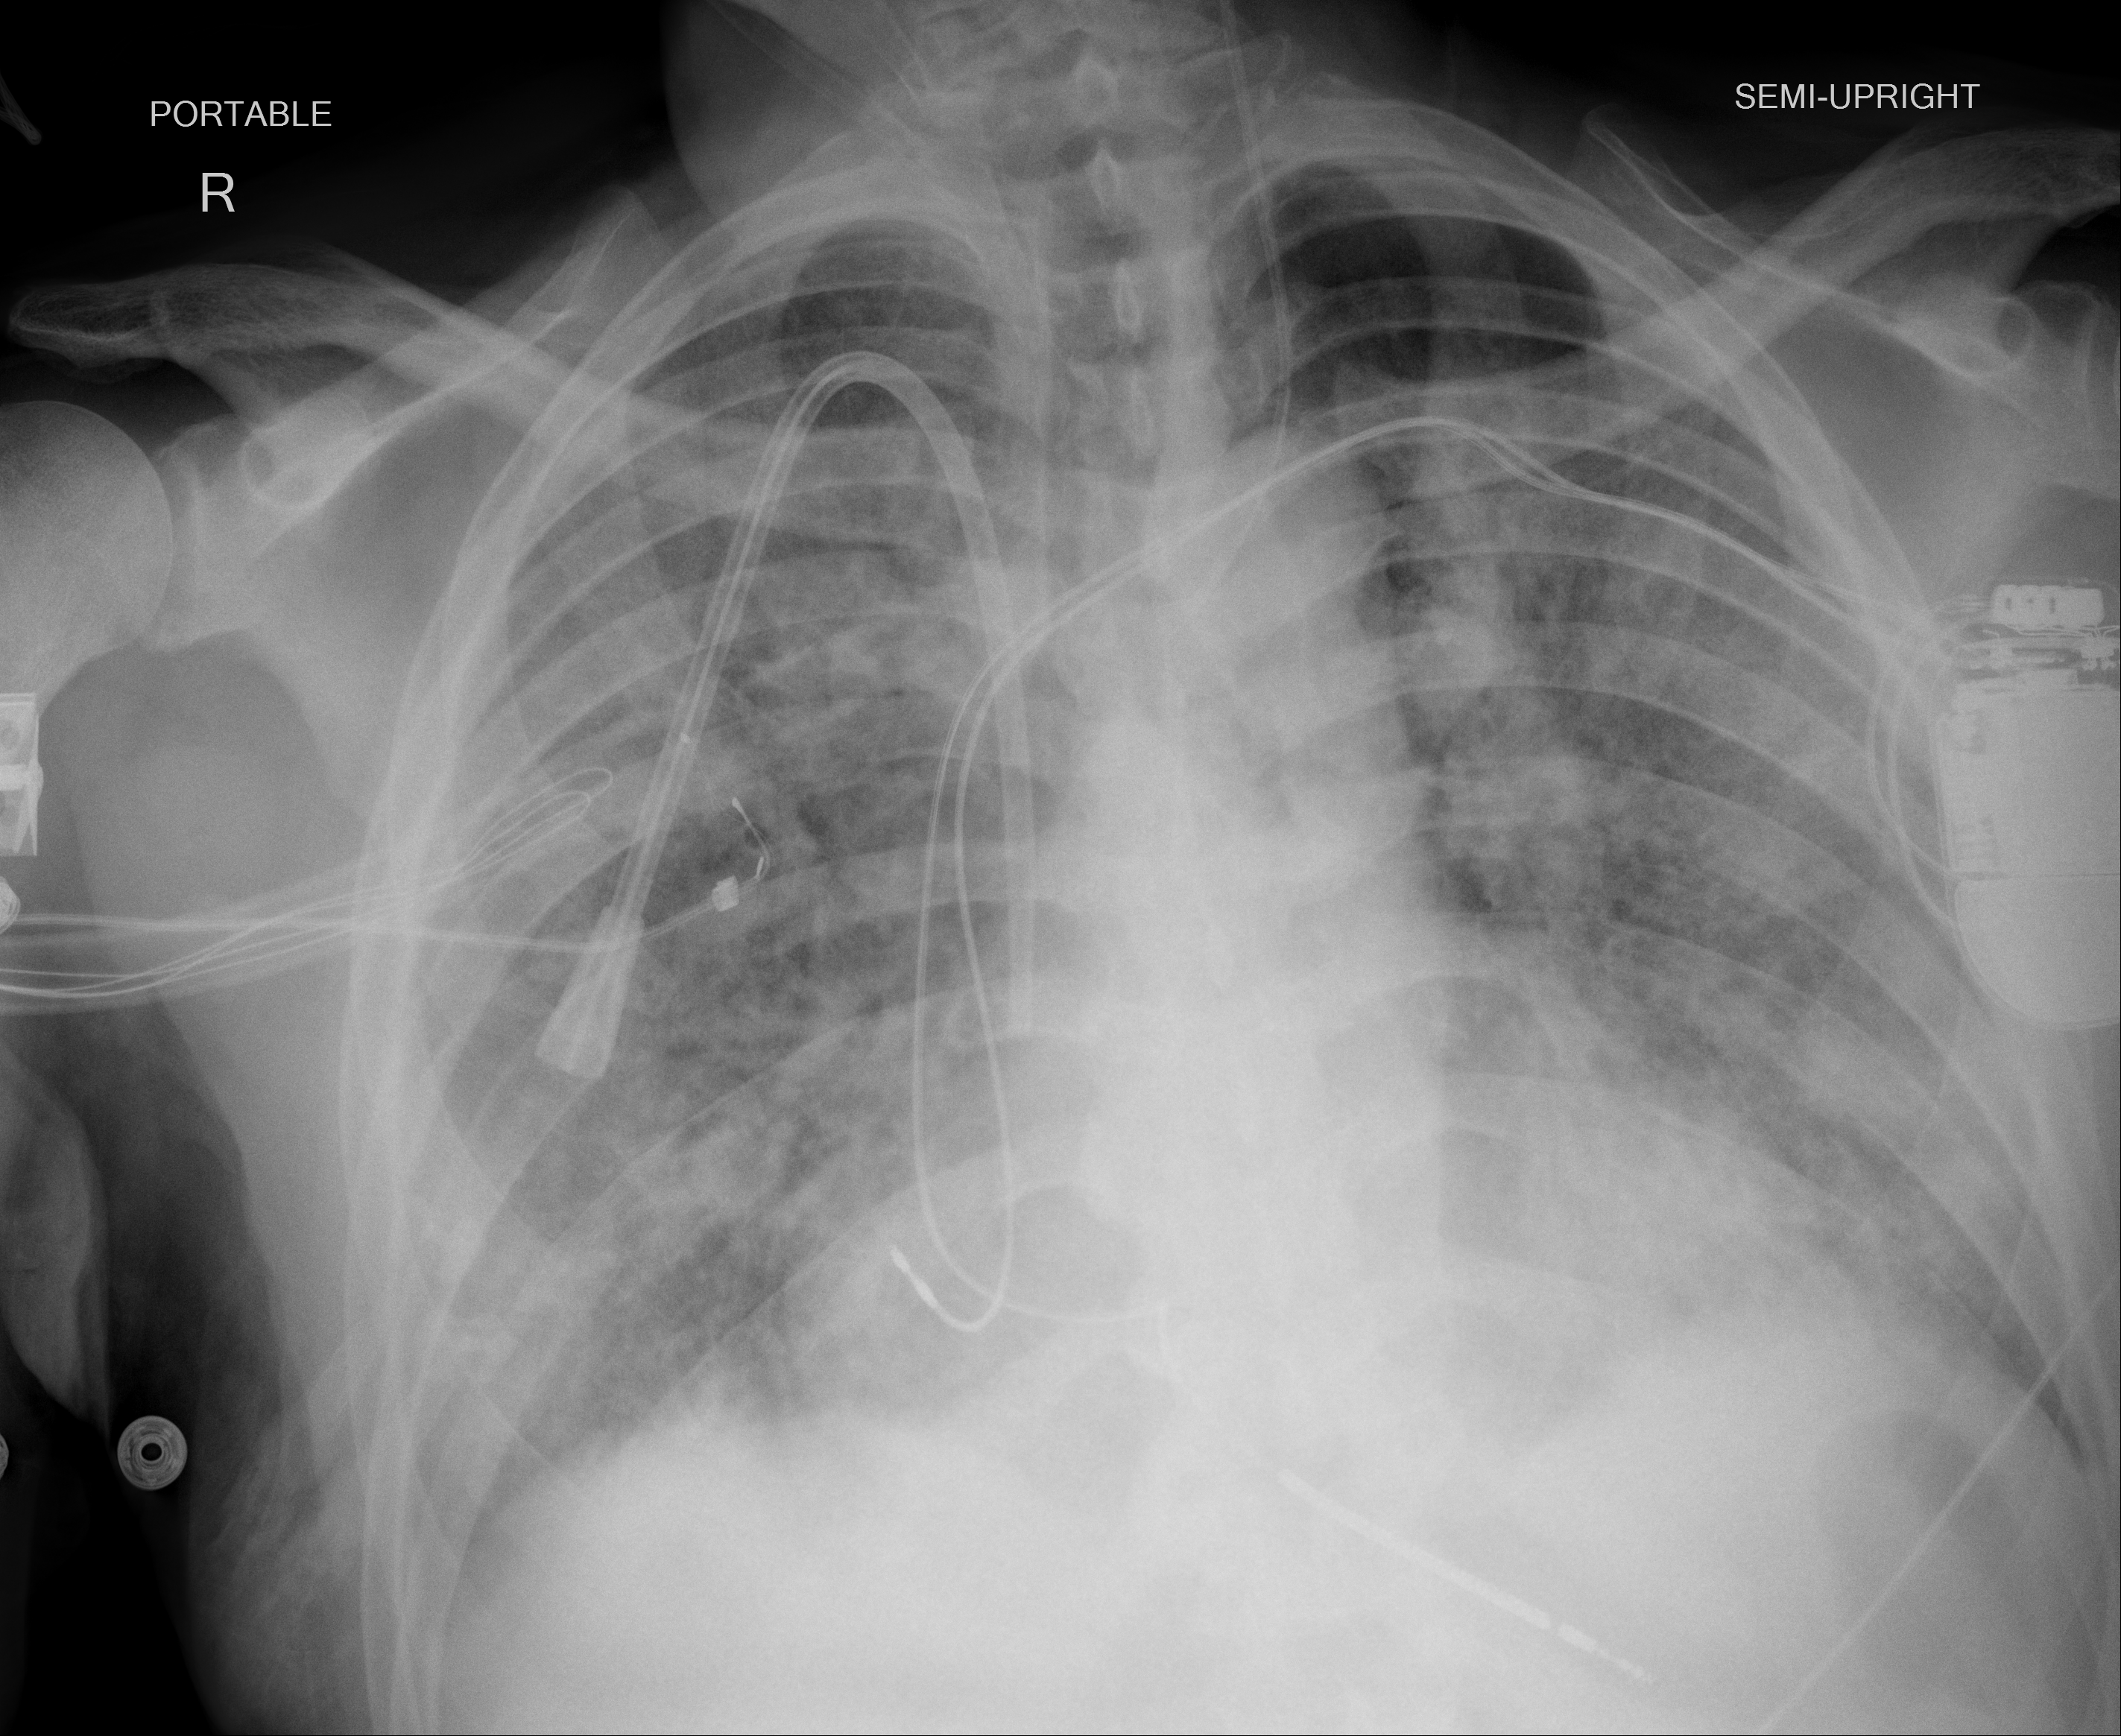
Portable chest radiograph, AP projection. Male patient, age 60 years; COVID-19 (test-positive).
Radiologist key findings (as recorded): worsening consolidative changes in both mid and lower lung zones. Minimal bilateral pleural effusions.